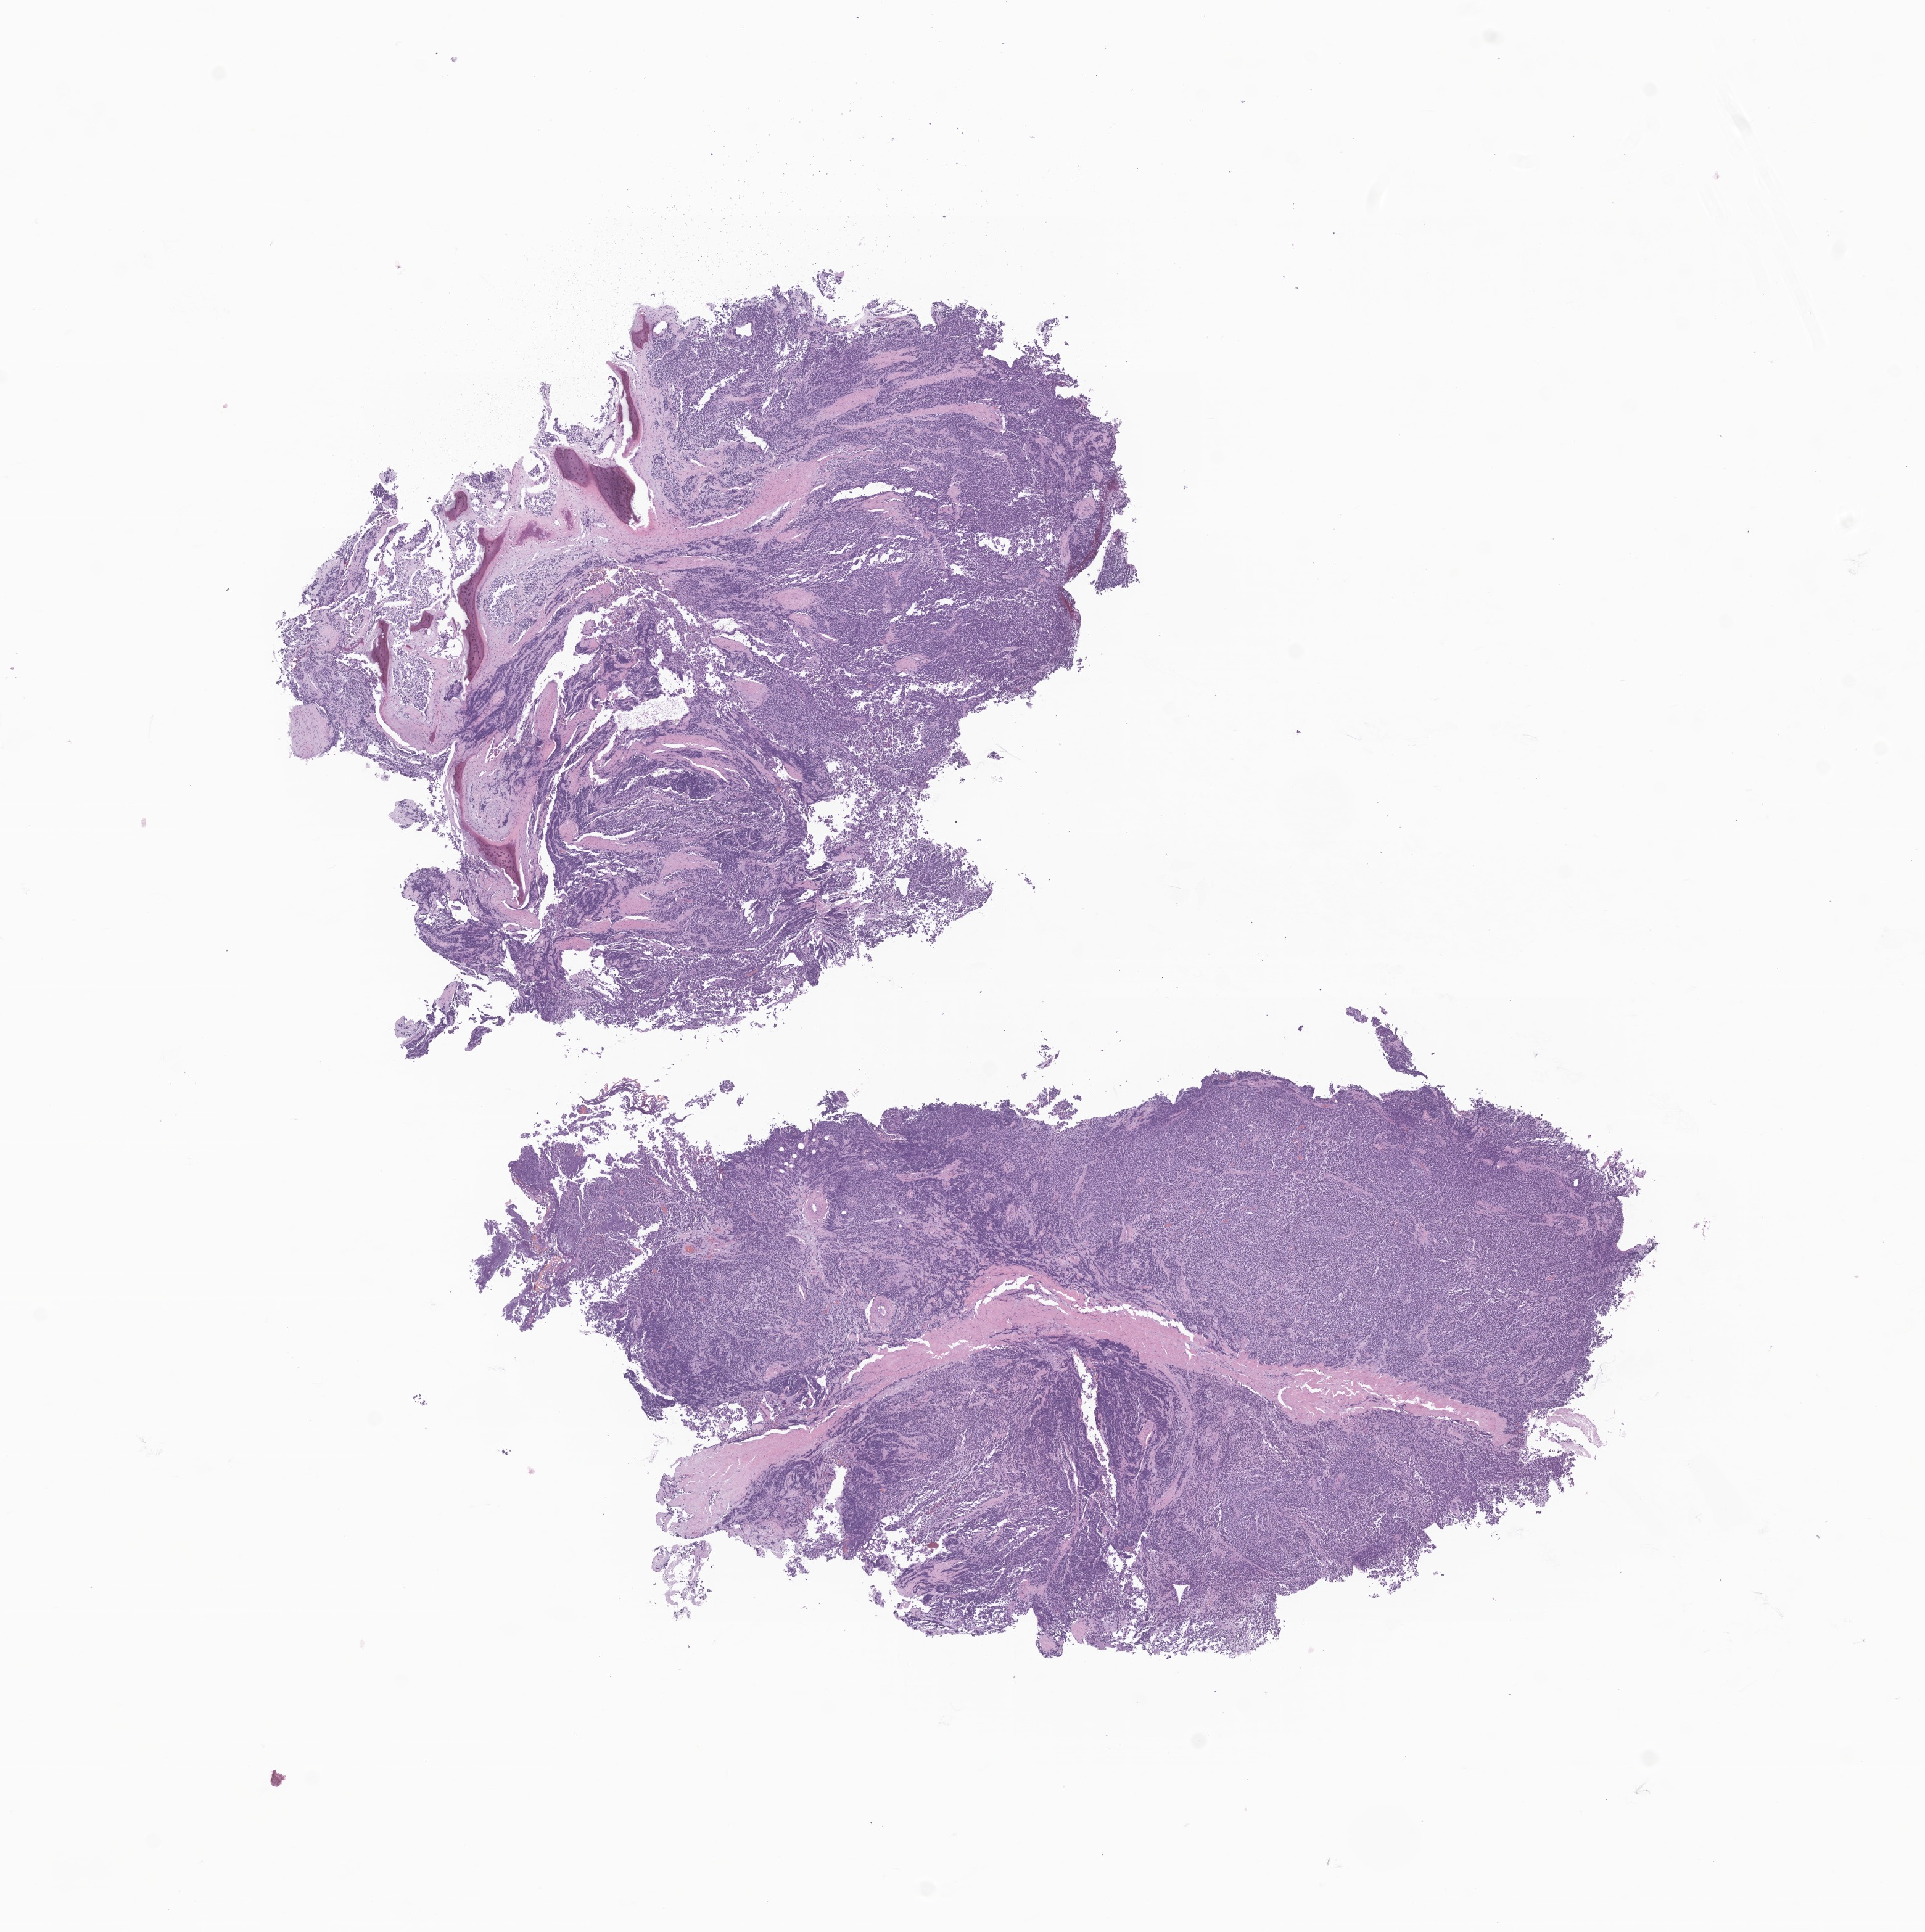
Whole-slide image, haematoxylin and eosin stain of tumor tissue from the soft tissue of upper extremity — low-resolution overview of the scanned area, about 13.2 x 13.2 mm. Formalin-fixed, paraffin-embedded (FFPE) tissue. Male patient, age 177 months (14 years 9 months).
- tissue or organ of origin (case record): connective, subcutaneous and other soft tissues of upper limb and shoulder
- diagnosis: Neuroblastoma, NOS